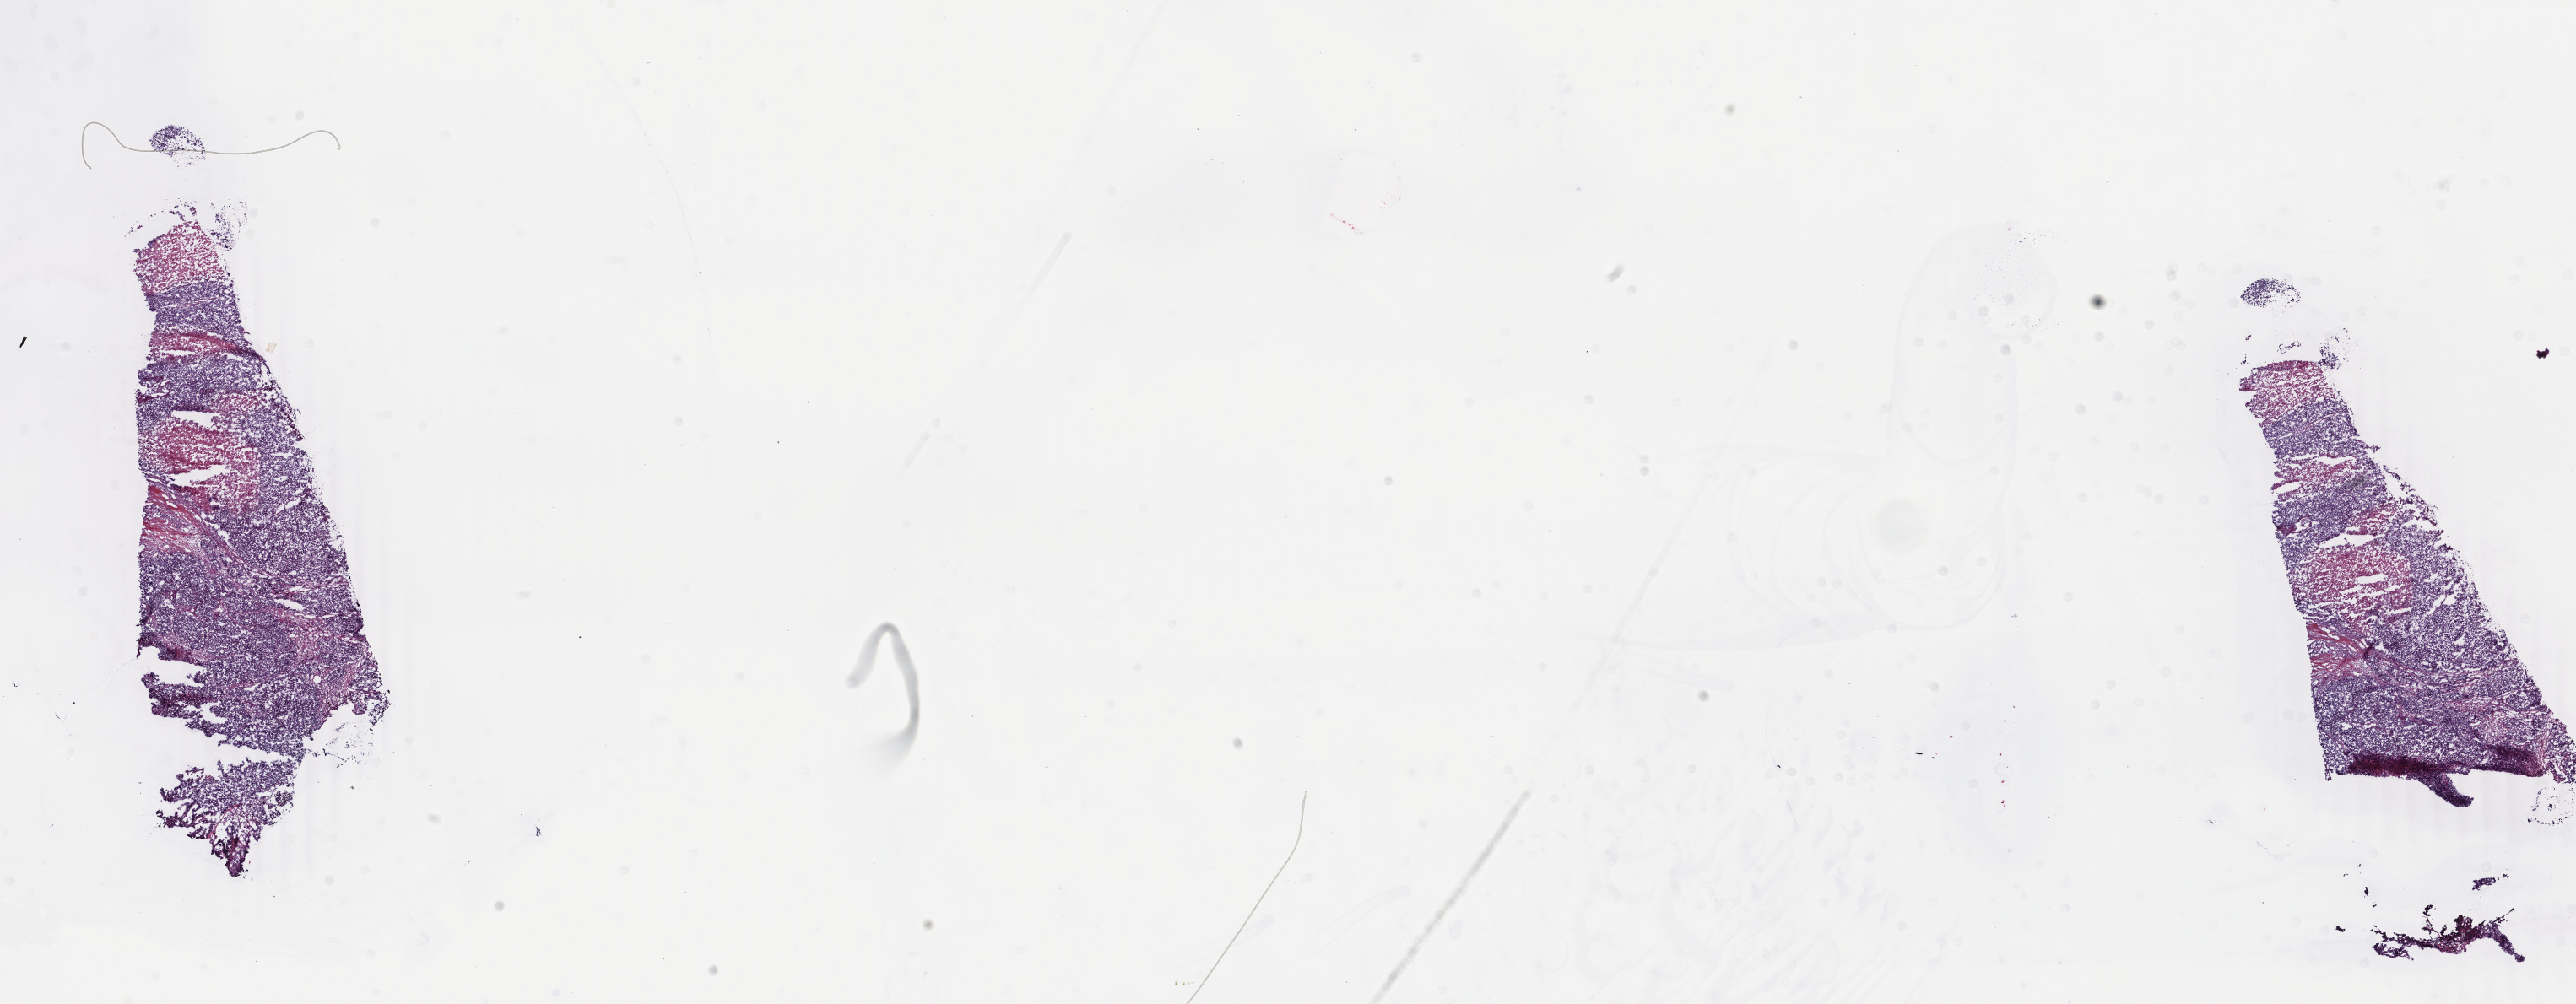
Digitized Hematoxylin and eosin (H&E) stained tissue section (whole slide), whole scanned area (about 24.3 x 9.5 mm, from a 40x scan) shown as a low-resolution overview, frozen section, primary tumour sample from the breast. Patient: female, age at initial diagnosis 58 years.
Pathologic diagnosis: Infiltrating duct carcinoma, NOS.